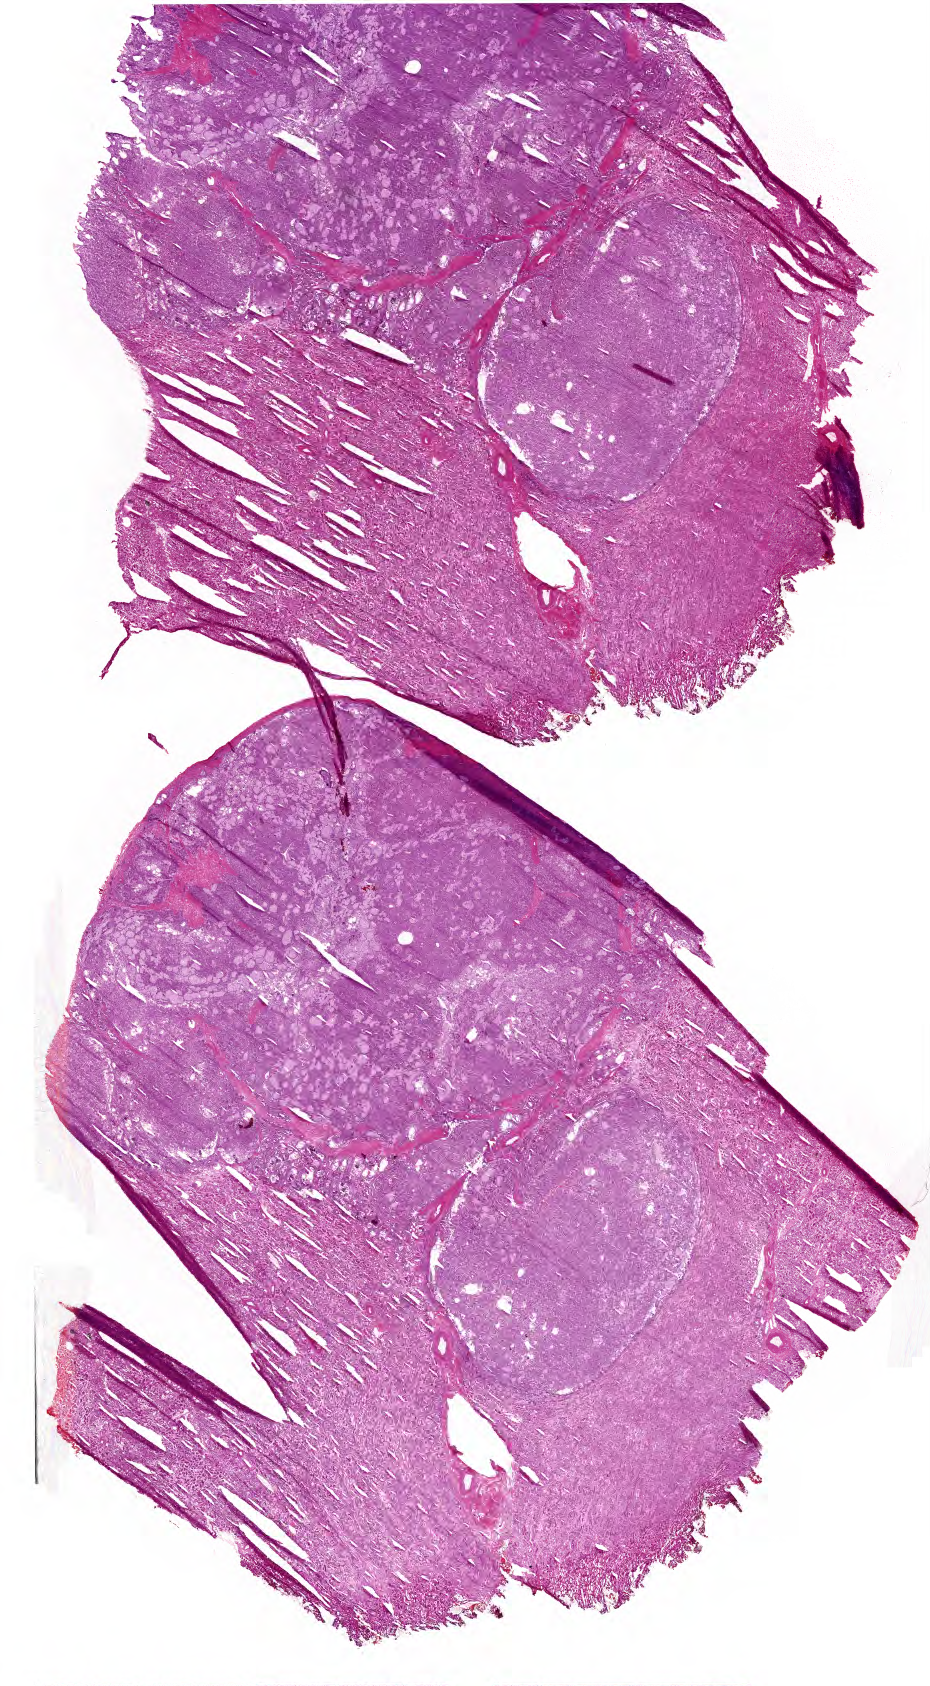
H&E whole-slide image, shown as a low-resolution overview of the whole scanned area (about 23.2 x 42.0 mm, from a 40x scan); formalin-fixed paraffin-embedded (FFPE) diagnostic section; sample: primary tumour, kidney. Male patient; age at initial diagnosis 49 years.
Pathologic diagnosis: Papillary adenocarcinoma, NOS.